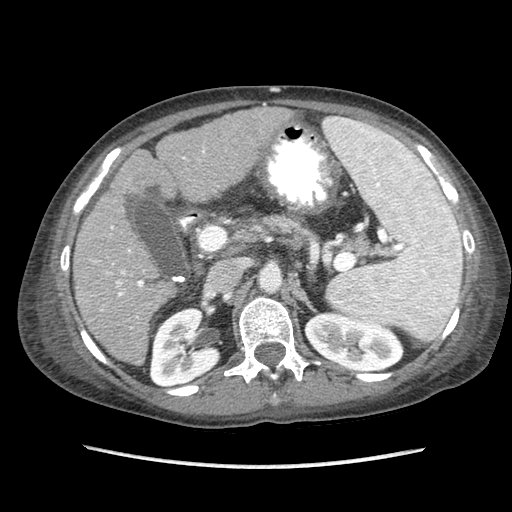
Contrast-enhanced abdominal CT (liver protocol), one axial slice; position 42 of 87 along the scan axis; reconstruction kernel STANDARD; 120 kVp; soft-tissue window (W 400 / L 40 HU); 2.5 mm slice thickness; 512 × 512 image matrix, field of view 340 × 340 mm. From the clinical record (not read from this slice): diagnosis: hepatocellular carcinoma (patient treated with transarterial chemoembolisation; whether this scan precedes or follows treatment is not stated here); TNM stage (as recorded): Stage-IIIB; Child-Pugh class: A; tumour differentiation: no biopsy.
Annotated regions visible in this slice (semi-automatically segmented with operator editing):
- liver parenchyma outside the tumour (the mass and vessels are separate outlines, so this box may not span the whole liver): bounding box [x1, y1, x2, y2] px = [74, 106, 292, 364]
- liver vessels: [97, 150, 205, 329]